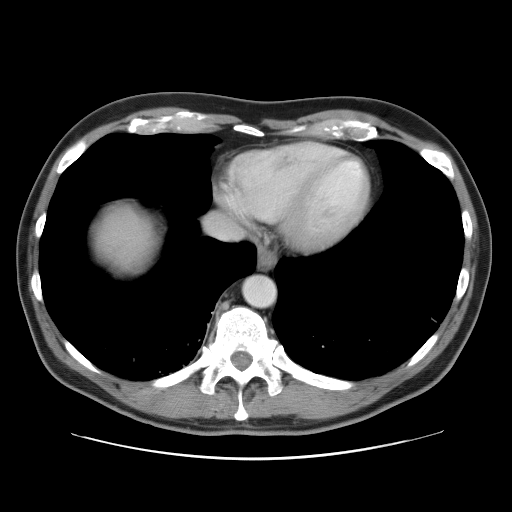
Contrast-enhanced abdominal CT, one axial slice; position 49 of 52 along the scan axis; reconstruction kernel STANDARD; 120 kVp; soft-tissue window (W 400 / L 40 HU); 512 × 512 image matrix. Male patient, age 70 years. Case-level facts recorded for this patient, not image findings: diagnosis: colorectal cancer liver metastases, imaged before liver resection; multiple liver metastases: yes; largest metastasis: 4 cm; disease in both lobes: yes.
Structures marked on this image (expert manual segmentation):
- hepatic veins: bounding box <225,193,250,215> (left, top, right, bottom; pixels)
- liver: <92,202,160,274>